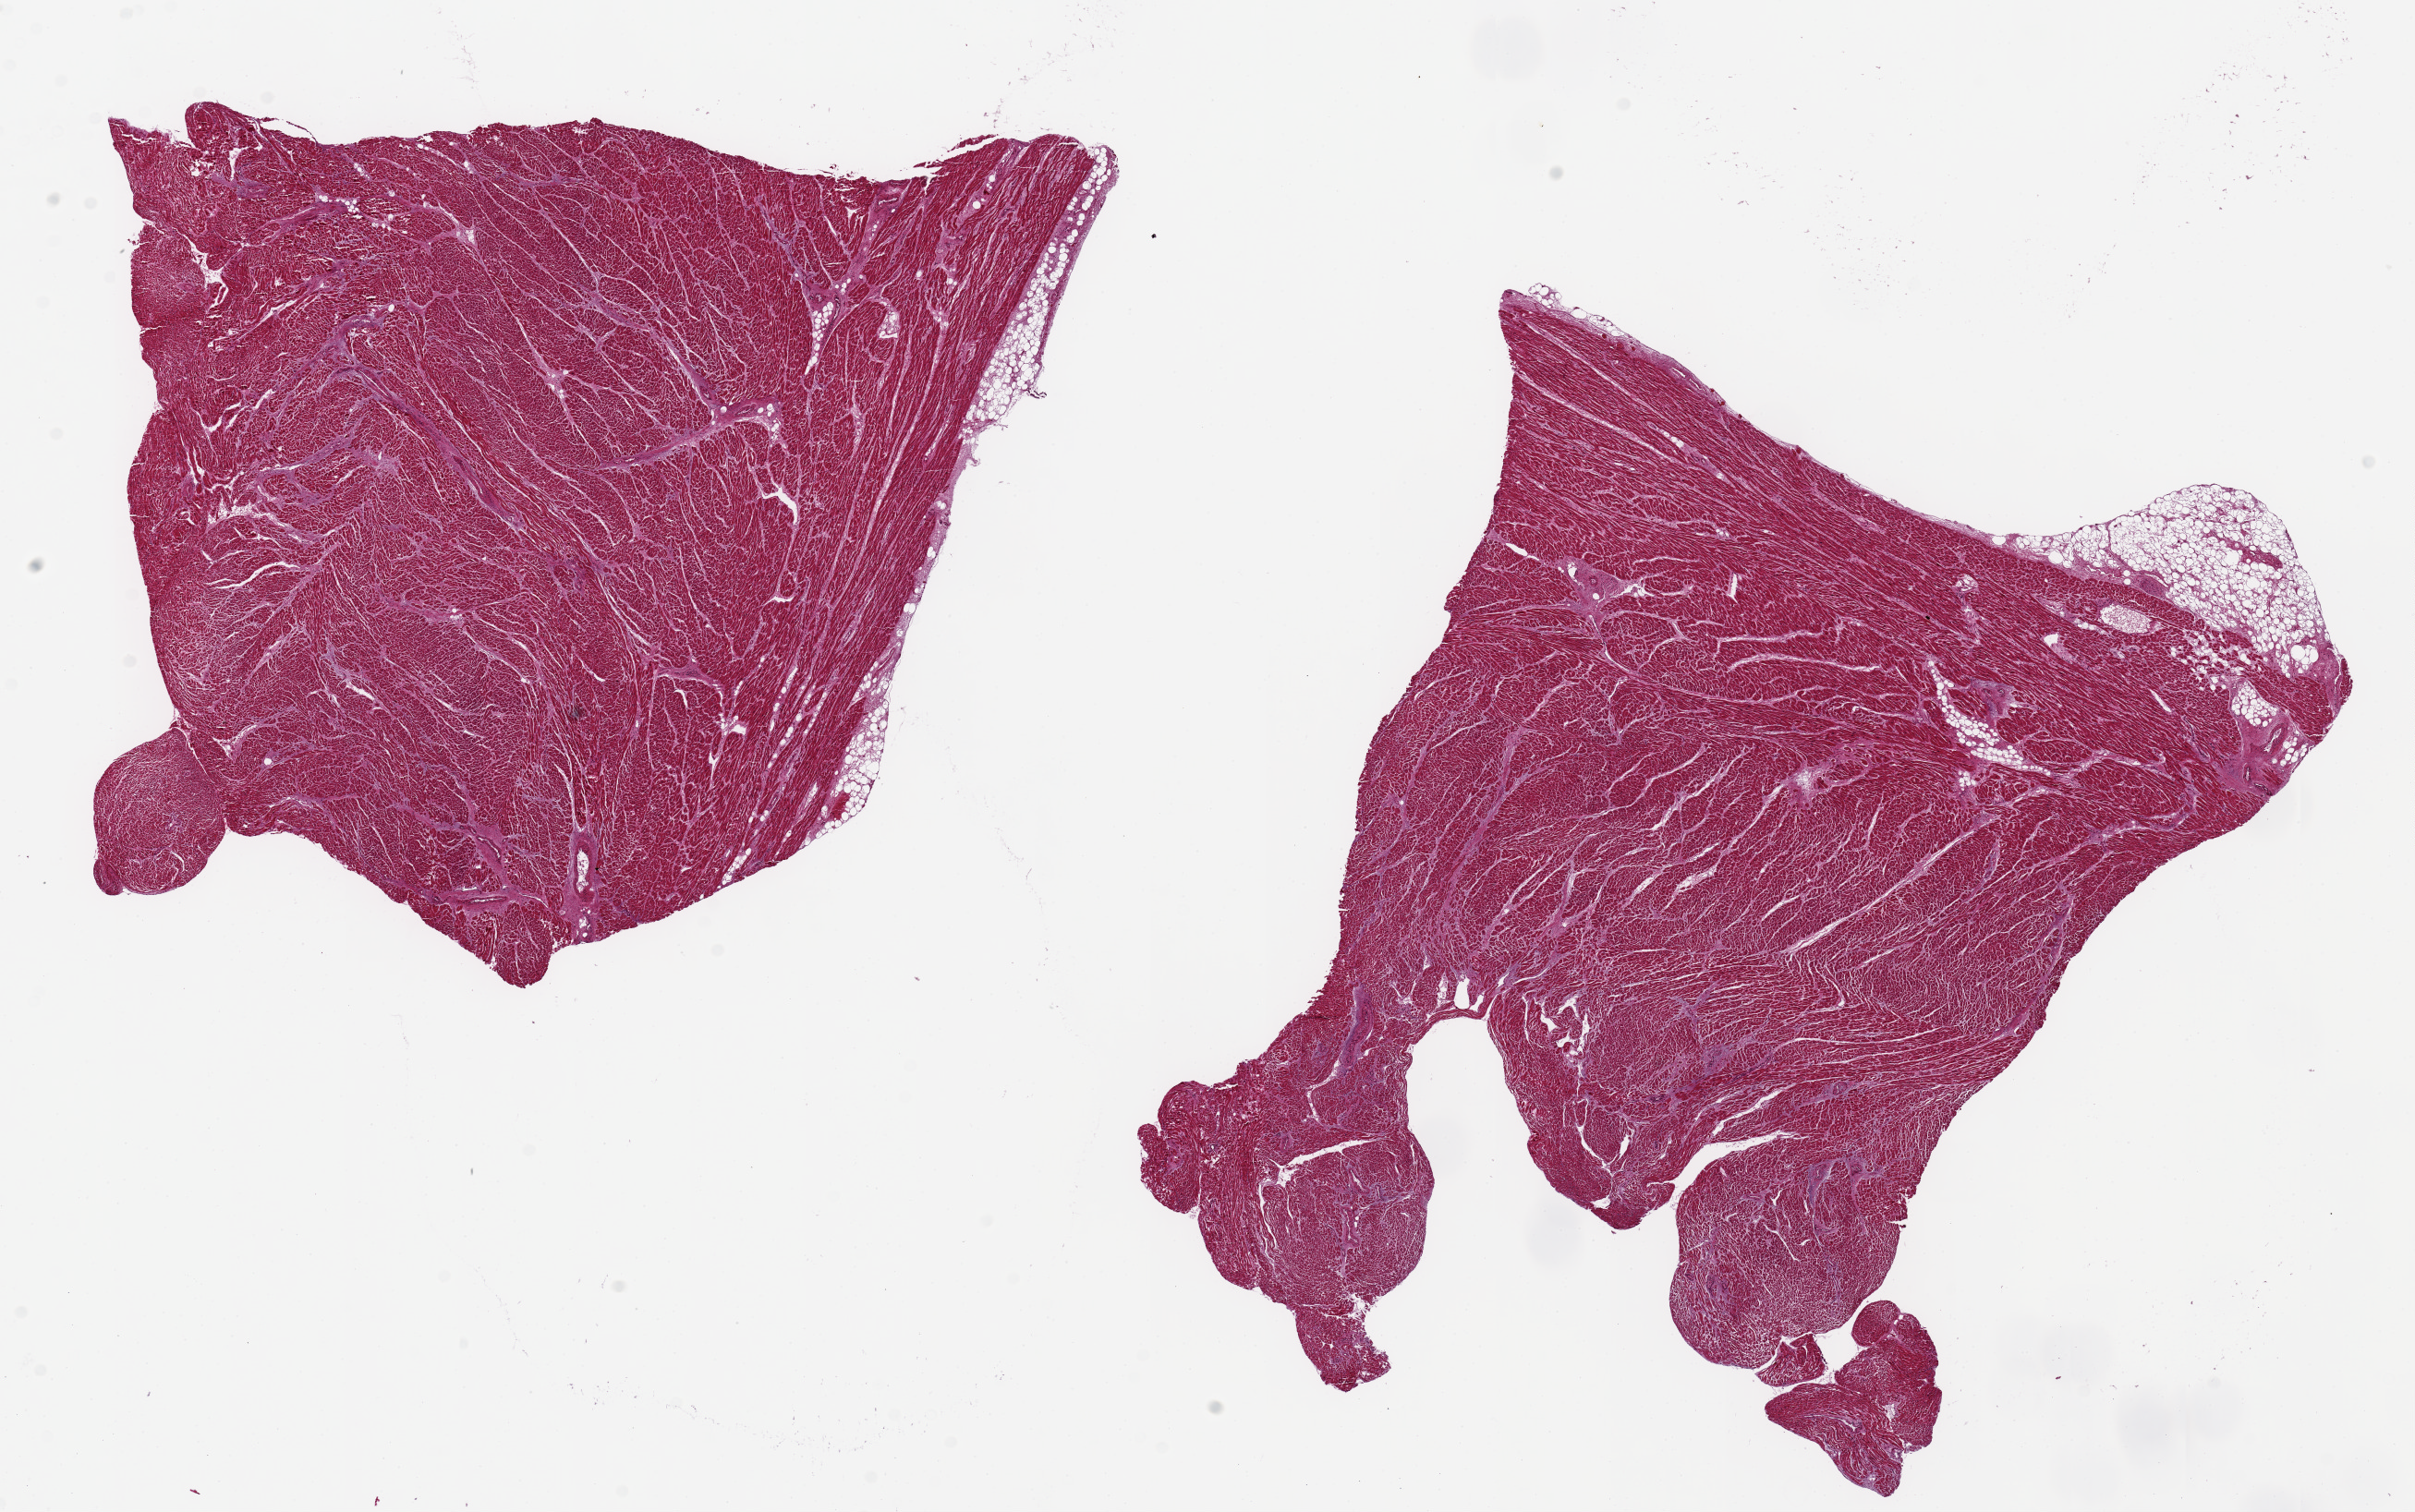
Whole-slide image, H&E stain — shown as a low-resolution overview of the whole scanned area (about 20.7 x 12.9 mm, slide scanned at 20x). PAXgene-fixed, paraffin-embedded tissue. Sampled site (target tissue): heart. Donor tissue sample.
Pathologist's review note for this sample: 2 pieces. 9x8 & 10x8mm; 10% external adipose.